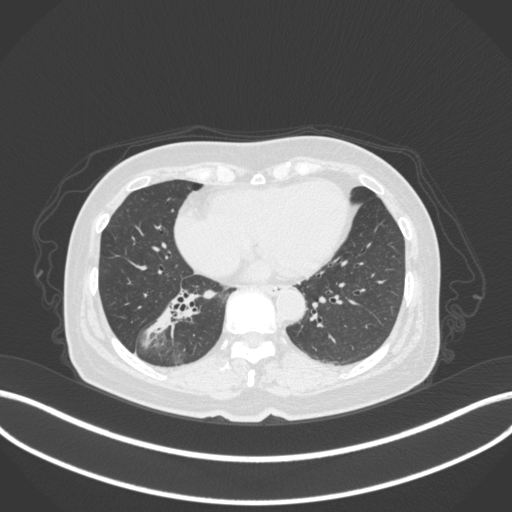
Chest CT, one axial slice. Position 147 of 429 along the scan axis. Reconstruction kernel B31f. 120 kVp. Lung window (W 1500 / L -600 HU). 1 mm slice thickness. 512 × 512 image matrix. Female patient, age 67 years. Case-level facts recorded for this patient, not image findings: clinical TNM (as recorded): T1c N1 M0.
Outlined on this slice (rectangle marked by the reading radiologist):
- lung tumour (recorded histology: adenocarcinoma): bounding box <141,293,204,349> (left, top, right, bottom; pixels)